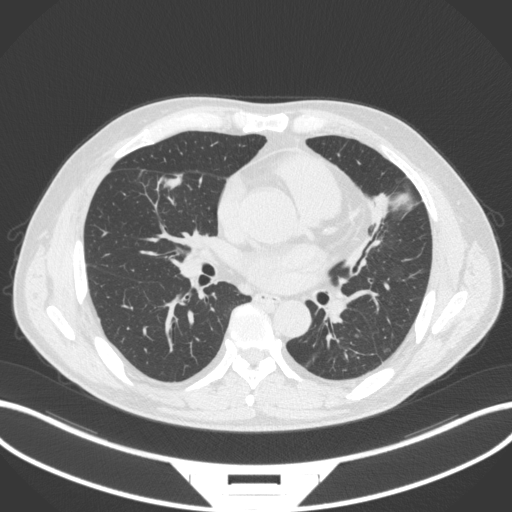
Chest CT, one axial slice. Position 151 of 399 along the scan axis. 120 kVp. Lung window (W 1500 / L -600 HU). 1 mm slice thickness. 512 × 512 image matrix. Patient: male, 59 years. Case-level facts recorded for this patient, not image findings: clinical TNM (as recorded): T2a N1 M0.
Outlined on this slice (bounding box drawn by a radiologist):
- lung tumour (recorded histology: adenocarcinoma): box from (x=161, y=171) to (x=184, y=195) px